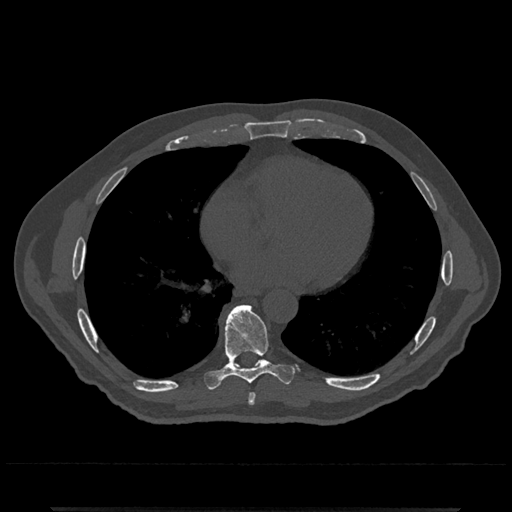
CT including the spine, one axial slice; position 668 of 797 along the scan axis; reconstruction kernel Br40s/3; 120 kVp; bone window (W 1800 / L 400 HU); 0.5 mm slice thickness; 512 × 512 image matrix, field of view 393 × 393 mm. Patient: male, 67 years. Case-level facts recorded for this patient, not image findings: primary cancer: prostate.
Structures marked on this image (semi-automatically segmented with operator editing):
- T7 vertebra: bounding box (x1, y1, x2, y2) in pixels: (248, 393, 256, 405)
- T8 vertebra: (204, 304, 295, 389)